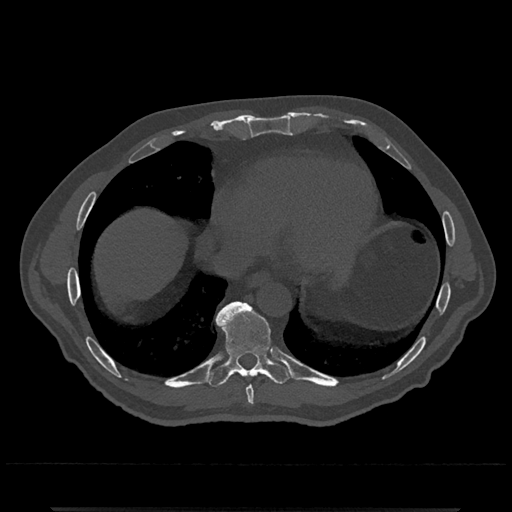
CT including the spine, one axial slice. Position 626 of 797 along the scan axis. Reconstruction kernel Br40s/3. 120 kVp. Bone window (W 1800 / L 400 HU). 512 × 512 image matrix, field of view 393 × 393 mm. Patient: male, 67 years. From the clinical record (not read from this slice): primary cancer: prostate.
Annotated regions visible in this slice (semi-automatic segmentation, software-assisted and operator-edited):
- T8 vertebra: box from (x=246, y=386) to (x=254, y=405) px
- T9 vertebra: (x=206, y=301)–(x=293, y=387)